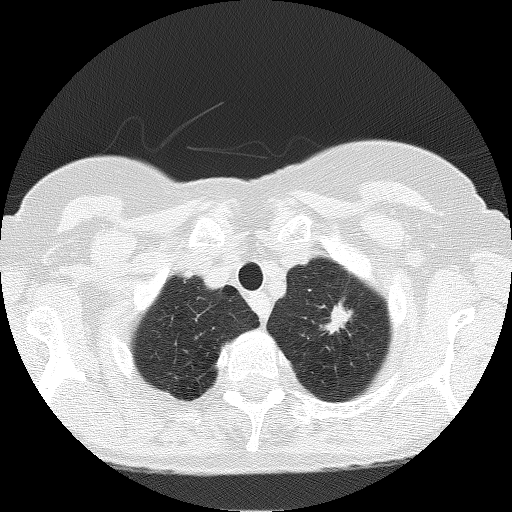
Low-dose screening chest CT, one axial slice; position 151 of 166 along the scan axis; reconstruction kernel FC51; lung window (W 1500 / L -600 HU); 512 × 512 image matrix.
Annotated regions visible in this slice (manually delineated by an expert):
- lesion 3 (nodule, upper lobe of left lung): bounding box (x1, y1, x2, y2) in pixels: (326, 304, 351, 334)